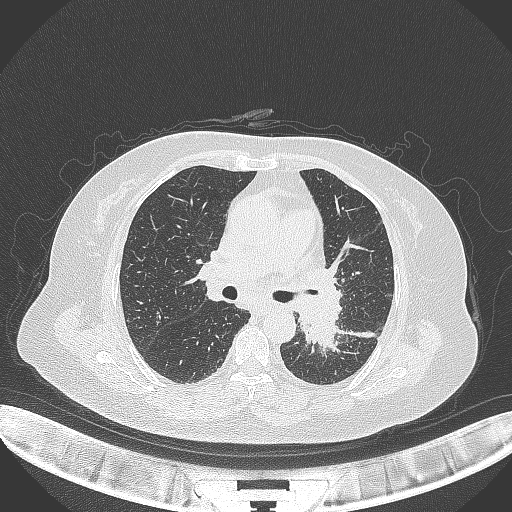
Chest CT, one axial slice. Slice 205 of 322 in the series (ordered by position). 120 kVp. Lung window (W 1500 / L -600 HU). 1 mm slice thickness. 512 × 512 image matrix. Female patient, age 69 years. Case-level facts recorded for this patient, not image findings: clinical TNM (as recorded): T2b N3 M1.
Annotated regions visible in this slice (bounding box drawn by a radiologist):
- lung tumour (recorded histology: adenocarcinoma): bounding box (x1, y1, x2, y2) in pixels: (297, 299, 340, 354)